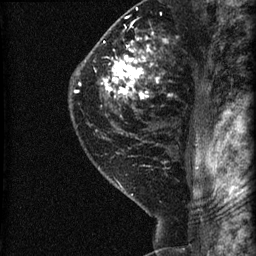
Breast MRI (dynamic contrast-enhanced), one sagittal slice. Slice 48 of 60 in the series (ordered by position). Dynamic contrast-enhanced series, image 2 of 3 at this slice position (ordered by acquisition). 1.5 T. TE 4.2 ms, TR 22.7 ms. 1.8 mm slice thickness. 256 × 256 image matrix, field of view 180 × 180 mm. Patient: female, 45 years. Case-level facts recorded for this patient, not image findings: setting: breast cancer imaged before/during neoadjuvant chemotherapy; receptor status: HR-positive, HER2-negative.
Structures marked on this image (semi-automatically segmented with operator editing):
- analysis volume of interest (the breast-tissue region the enhancement analysis was run in; not a lesion): bounding box <74,11,205,140> (left, top, right, bottom; pixels)
- tumour enhancement mask (voxels above the 90 % enhancement threshold inside the analysis volume of interest): <74,36,167,99>